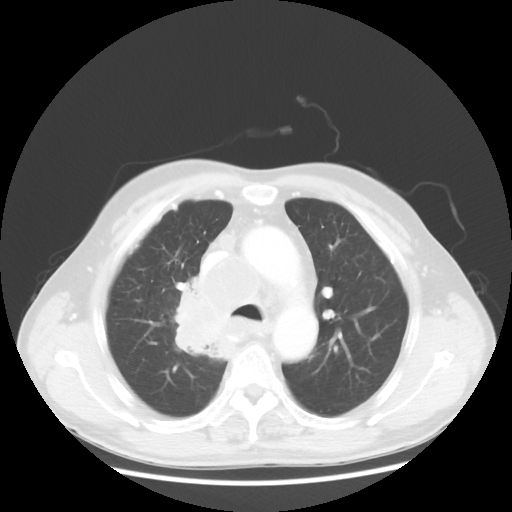
Chest CT, one axial slice; position 85 of 124 along the scan axis; reconstruction kernel STANDARD; 100 kVp; lung window (W 1500 / L -600 HU); 5 mm slice thickness; 512 × 512 image matrix, field of view 382 × 382 mm. Patient: male, 64 years. From the clinical record (not read from this slice): clinical TNM (as recorded): T3 N3 M0; histopathological grade: G3.
Structures marked on this image (rectangle marked by the reading radiologist):
- lung tumour (recorded histology: small cell carcinoma): box from (x=162, y=284) to (x=227, y=371) px